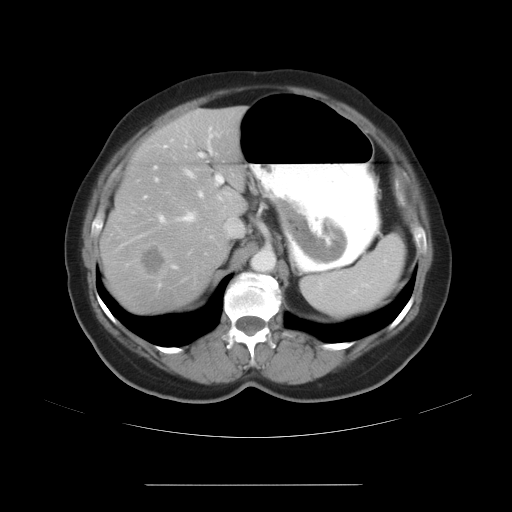
Contrast-enhanced abdominal CT, one axial slice; position 19 of 27 along the scan axis; 120 kVp; intravenous contrast given; soft-tissue window (W 400 / L 40 HU); 512 × 512 image matrix, field of view 440 × 440 mm. Female patient, age 58 years. Case-level facts recorded for this patient, not image findings: diagnosis: colorectal cancer liver metastases, imaged before liver resection; multiple liver metastases: yes; largest metastasis: 1.9 cm; disease in both lobes: yes.
Annotated regions visible in this slice (manually delineated by an expert):
- hepatic veins: box from (x=114, y=170) to (x=239, y=252) px
- liver: (x=103, y=109)–(x=245, y=309)
- planned liver remnant (the part of the liver to remain after resection): (x=117, y=120)–(x=245, y=223)
- portal vein (with intrahepatic branches): (x=135, y=126)–(x=238, y=269)
- liver metastasis: (x=141, y=248)–(x=166, y=276)